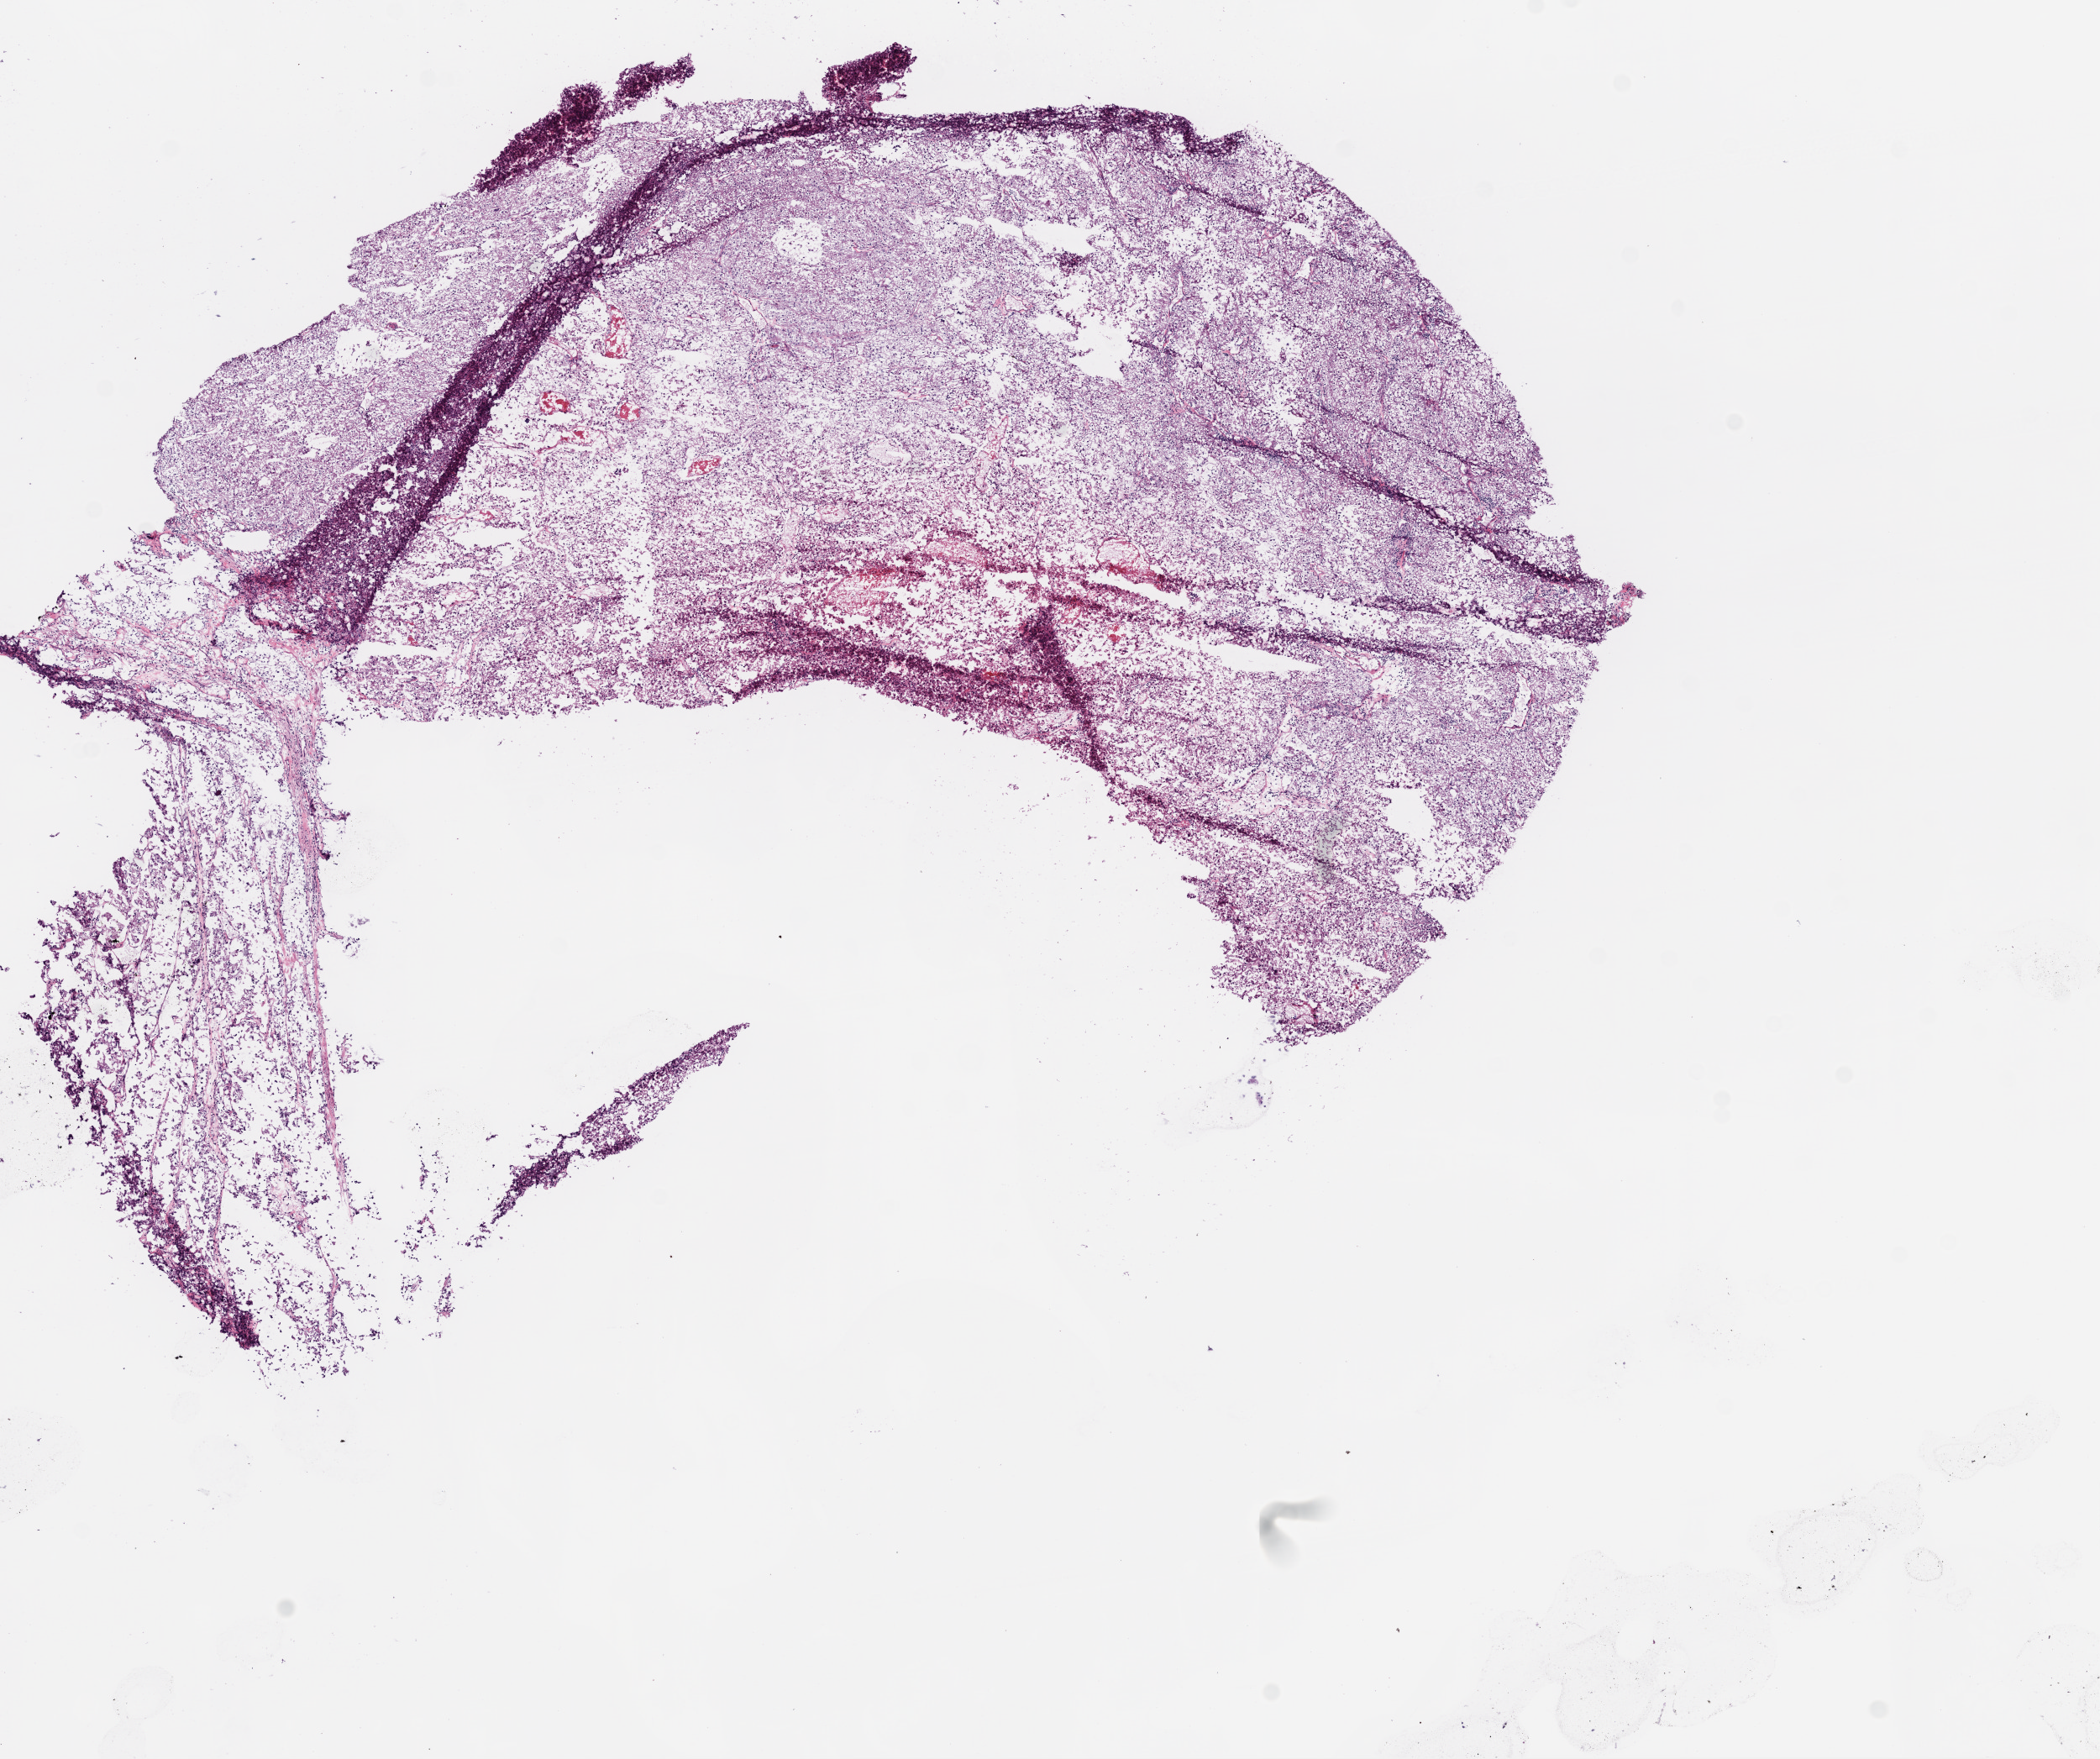
Digitized H&E-stained tissue section (whole slide) — shown as a low-resolution overview of the whole scanned area (about 10.0 x 8.4 mm). Frozen section from the top of the tissue portion. Sample: primary tumour, kidney. Patient: male, age at initial diagnosis 41 years. Histologic grade: G4 (undifferentiated). Pathologist review of this section (percent, as recorded): tumour cells 90%, tumour nuclei 80%, normal cells 0%, stromal cells 5%, necrosis 5%.
* pathologic diagnosis: Clear cell adenocarcinoma, NOS
* TNM: T2a N0 M0
* AJCC pathologic stage: II